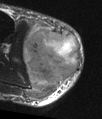
MRI of an extremity soft-tissue mass, one axial slice. Position 23 of 48 along the scan axis. T2-weighted fat-saturated. MR volume resampled by the dataset authors to the PET/CT grid (not the native acquisition matrix). 102 × 119 image matrix, field of view 100 × 116 mm. Male patient. From the clinical record (not read from this slice): histological type: pleiomorphic liposarcoma; grade: high; site of the primary tumour: right calf.
Outlined on this slice (expert contour drawn on MRI and transferred to this co-registered scan by the dataset authors):
- gross tumour volume including surrounding oedema: bounding box [x1, y1, x2, y2] px = [23, 21, 81, 100]
- gross tumour volume (mass): [25, 28, 81, 86]